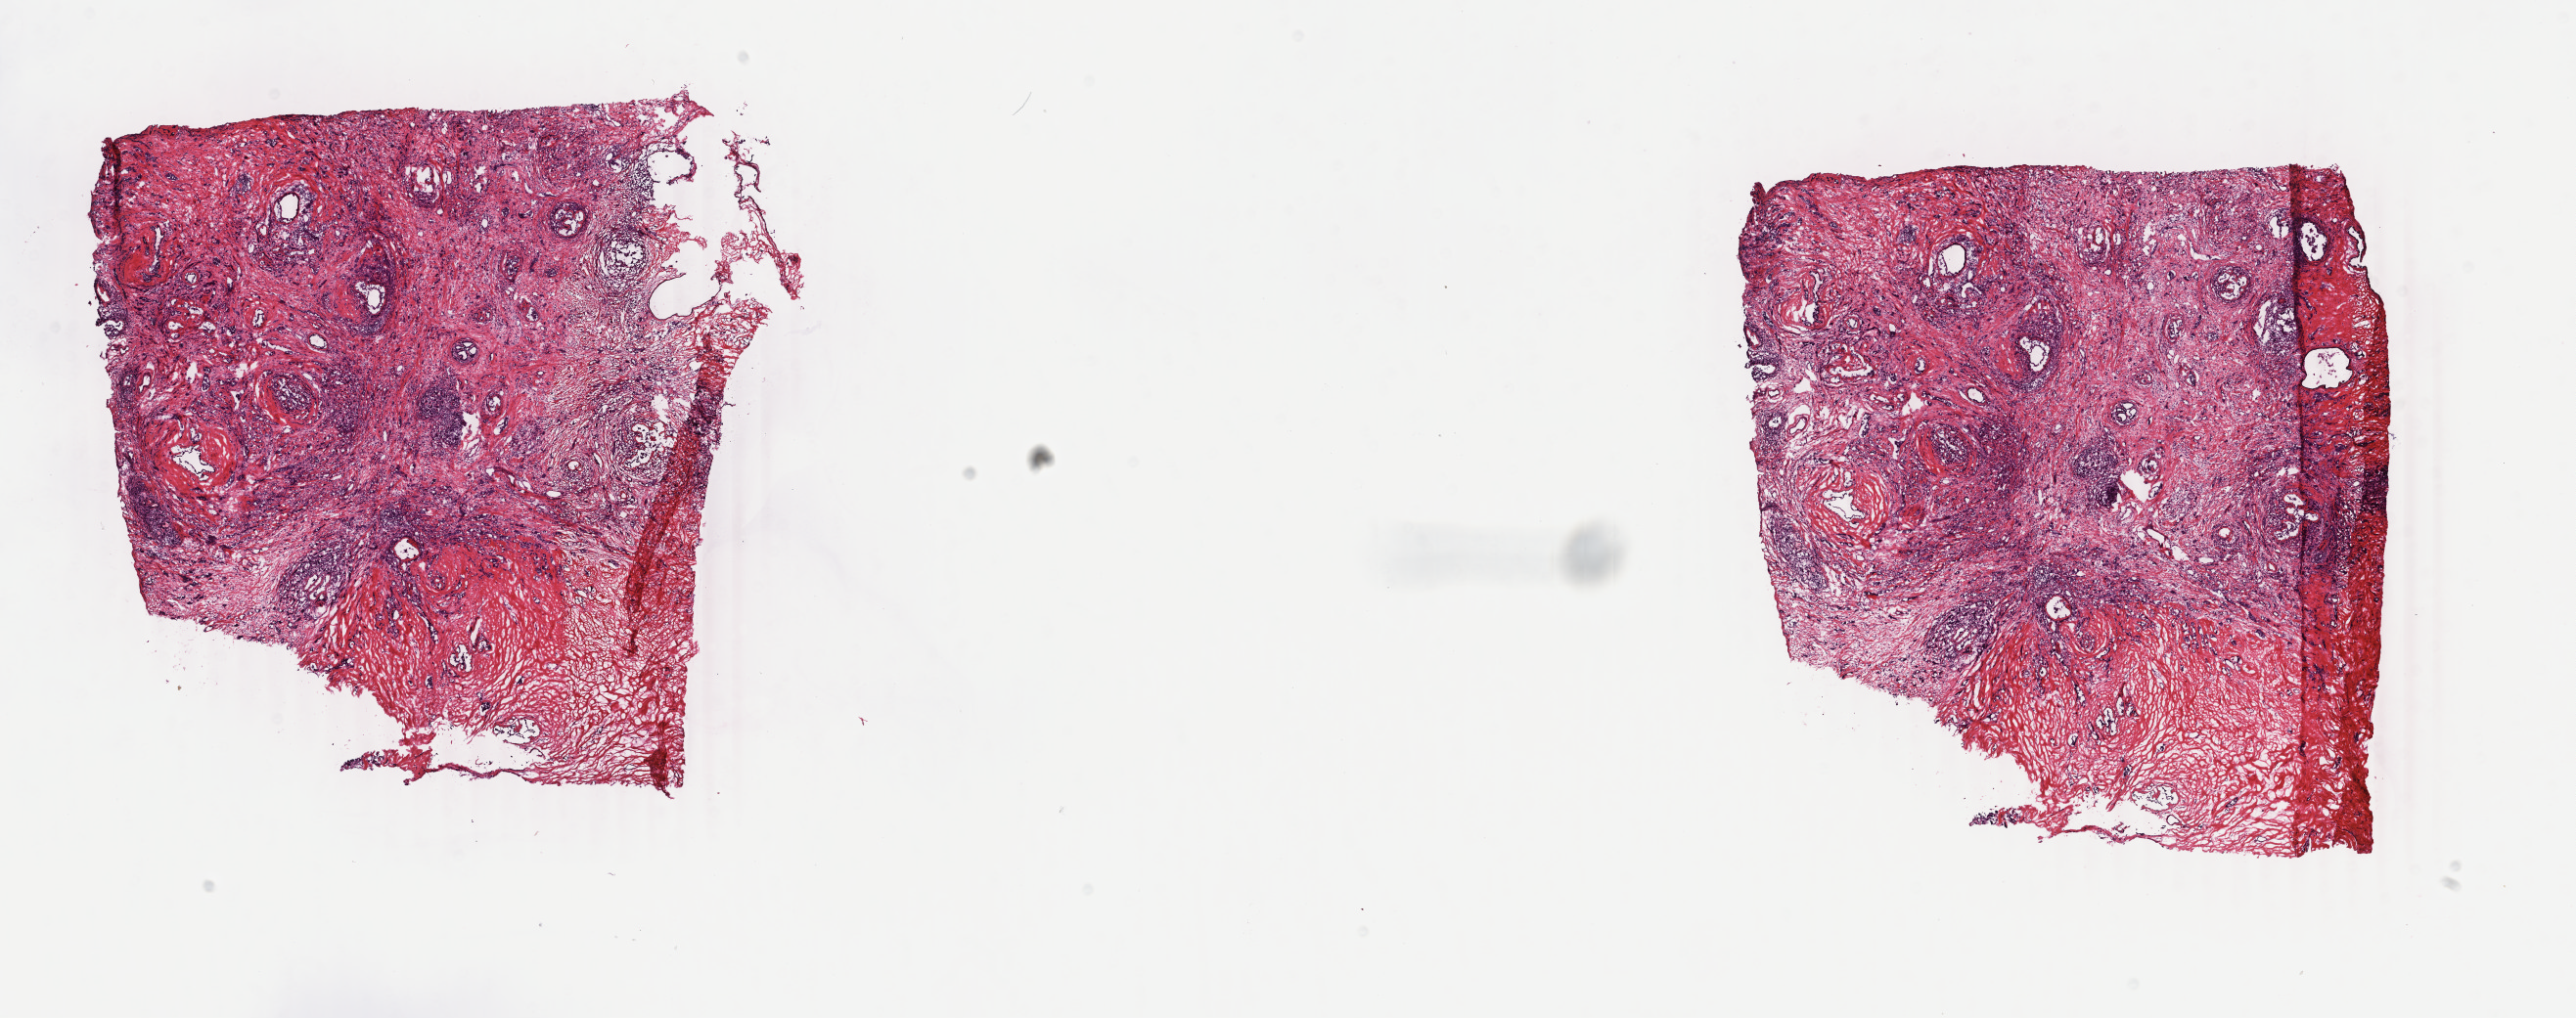
H&E whole-slide image, shown as a low-resolution overview of the whole scanned area (about 20.9 x 8.3 mm); frozen section from the top of the tissue portion; primary tumour sample from the breast. Female, age 42 years at initial diagnosis. Slide review estimates, as recorded: tumour cells 85%, tumour nuclei 70%.
Pathologic diagnosis: Infiltrating duct and lobular carcinoma.